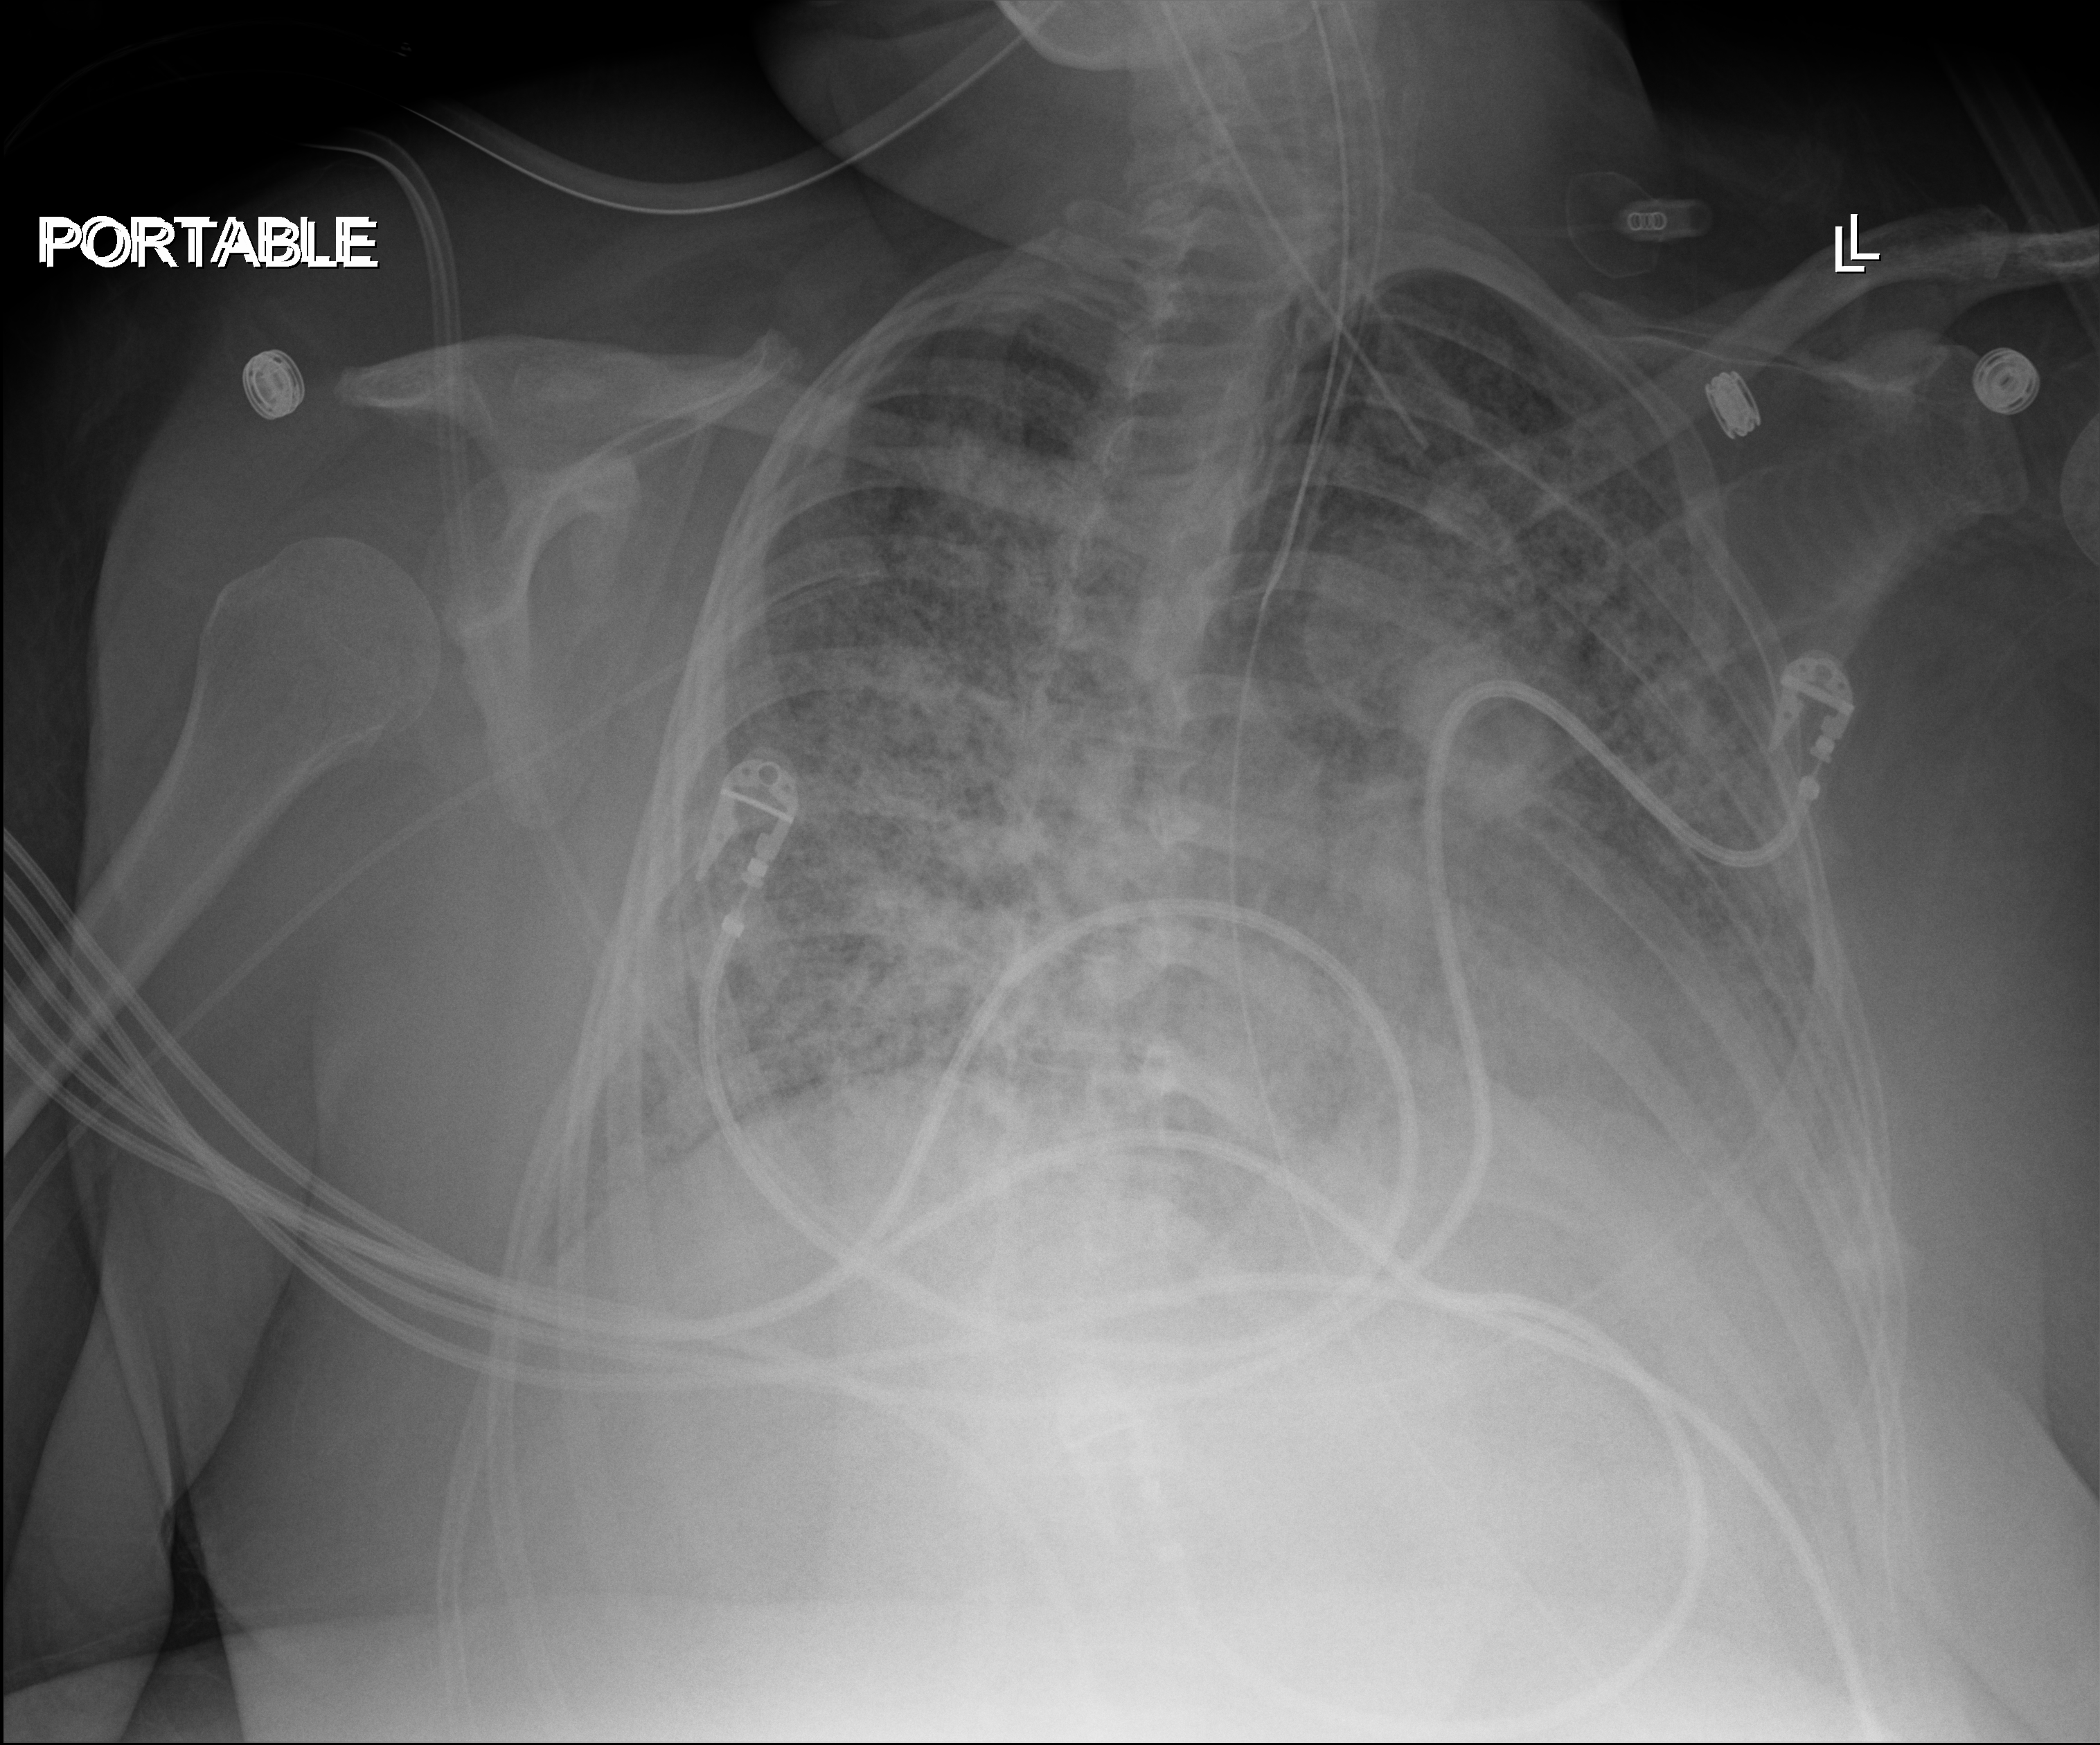
Bedside chest radiograph (digital radiography), anteroposterior (AP) projection. Female patient hospitalised with COVID-19, age 18–59 years.
From the hospital-stay record, not from the radiograph (when in the stay this image was taken is not recorded): admitted to intensive care during this hospital stay: yes; mechanically ventilated during this hospital stay: yes.